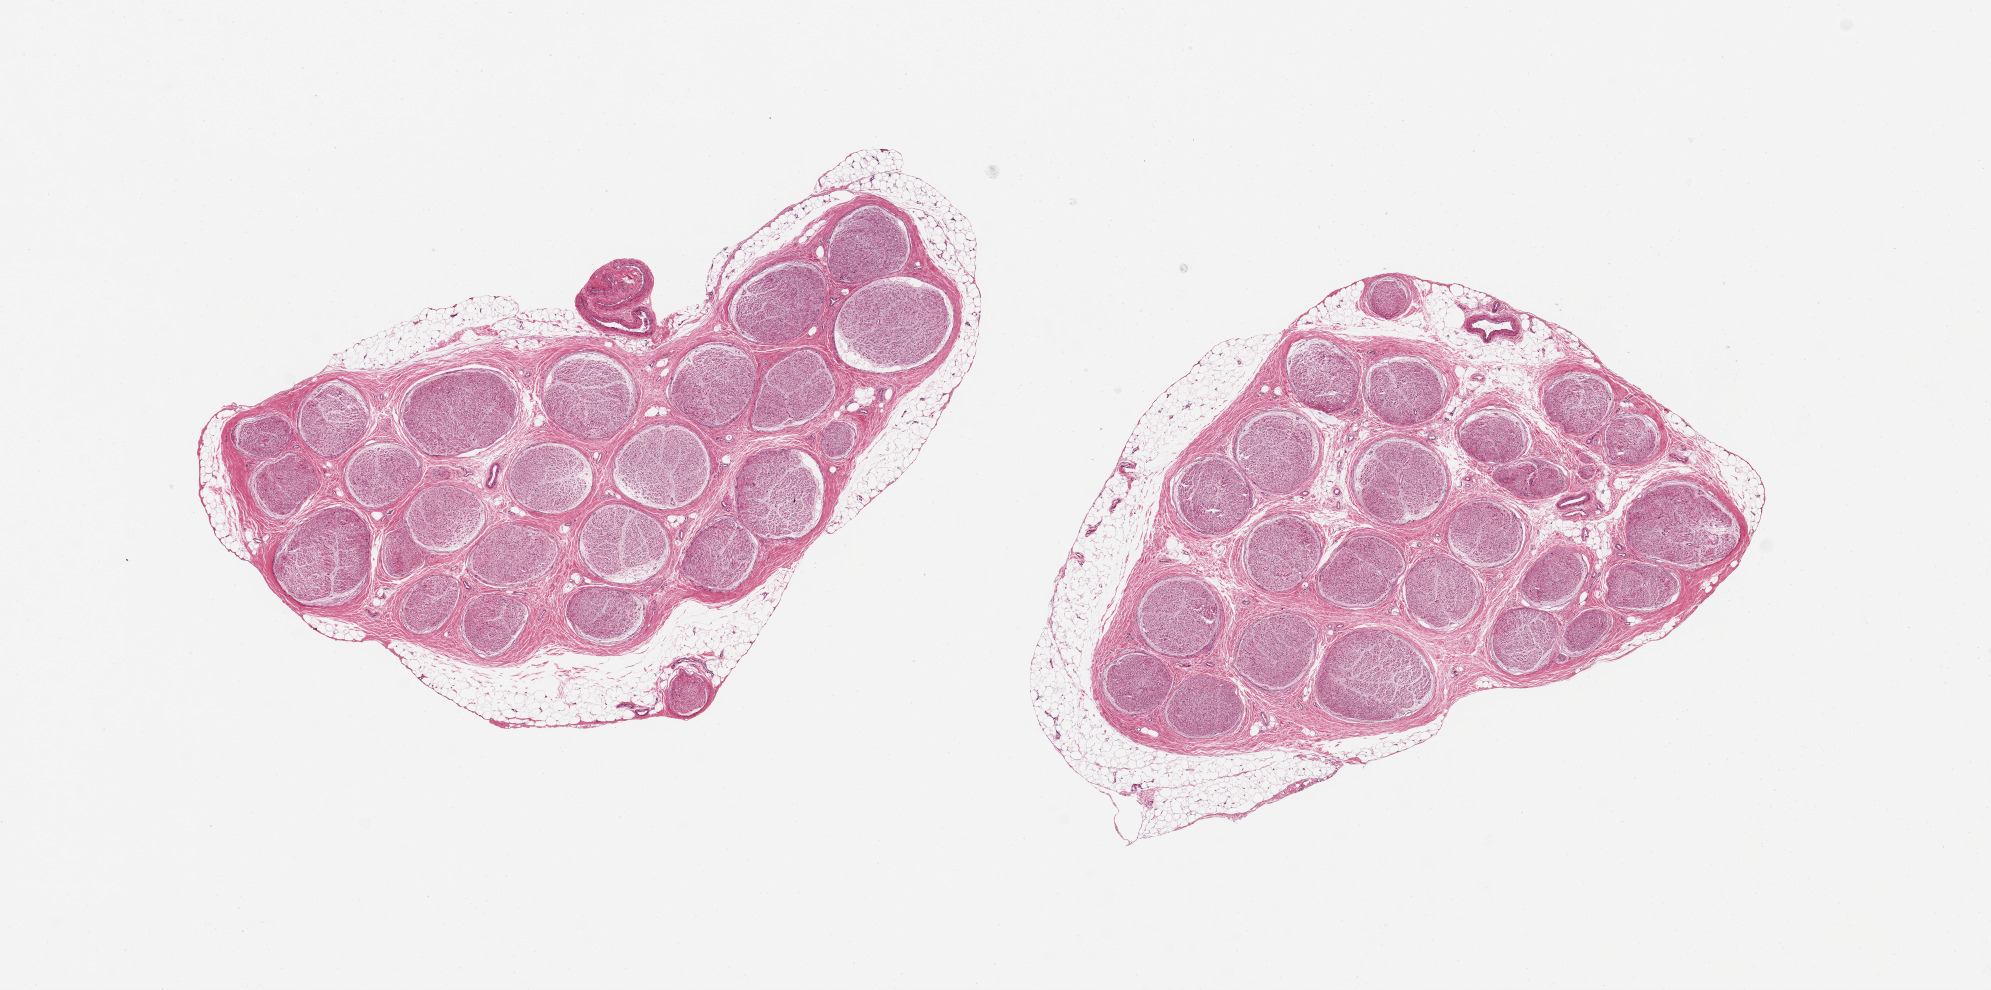
Digitized haematoxylin and eosin-stained section, shown as a low-resolution overview of the whole scanned area (about 15.8 x 7.8 mm). PAXgene-fixed, paraffin-embedded tissue. Sampled site (target tissue): tibial nerve. Donor tissue sample. Female donor.
* review note (as recorded): 2 ~6.5x3.5mm aliquots. ~0.5mm rim of fat around both